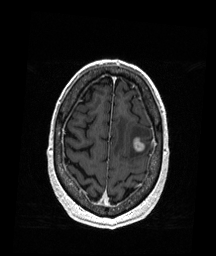
Brain MRI from a brain-tumour surgery series, one axial slice. Slice 44 of 176 in the series (ordered by position). T1-weighted post-contrast. 216 × 256 image matrix. Case-level facts recorded for this patient, not image findings: histopathology: Metastatic Melanoma; tumour location: Left Frontal.
Outlined on this slice (outlined manually by an expert reader):
- tumour: bounding box (x1, y1, x2, y2) in pixels: (132, 139, 145, 152)